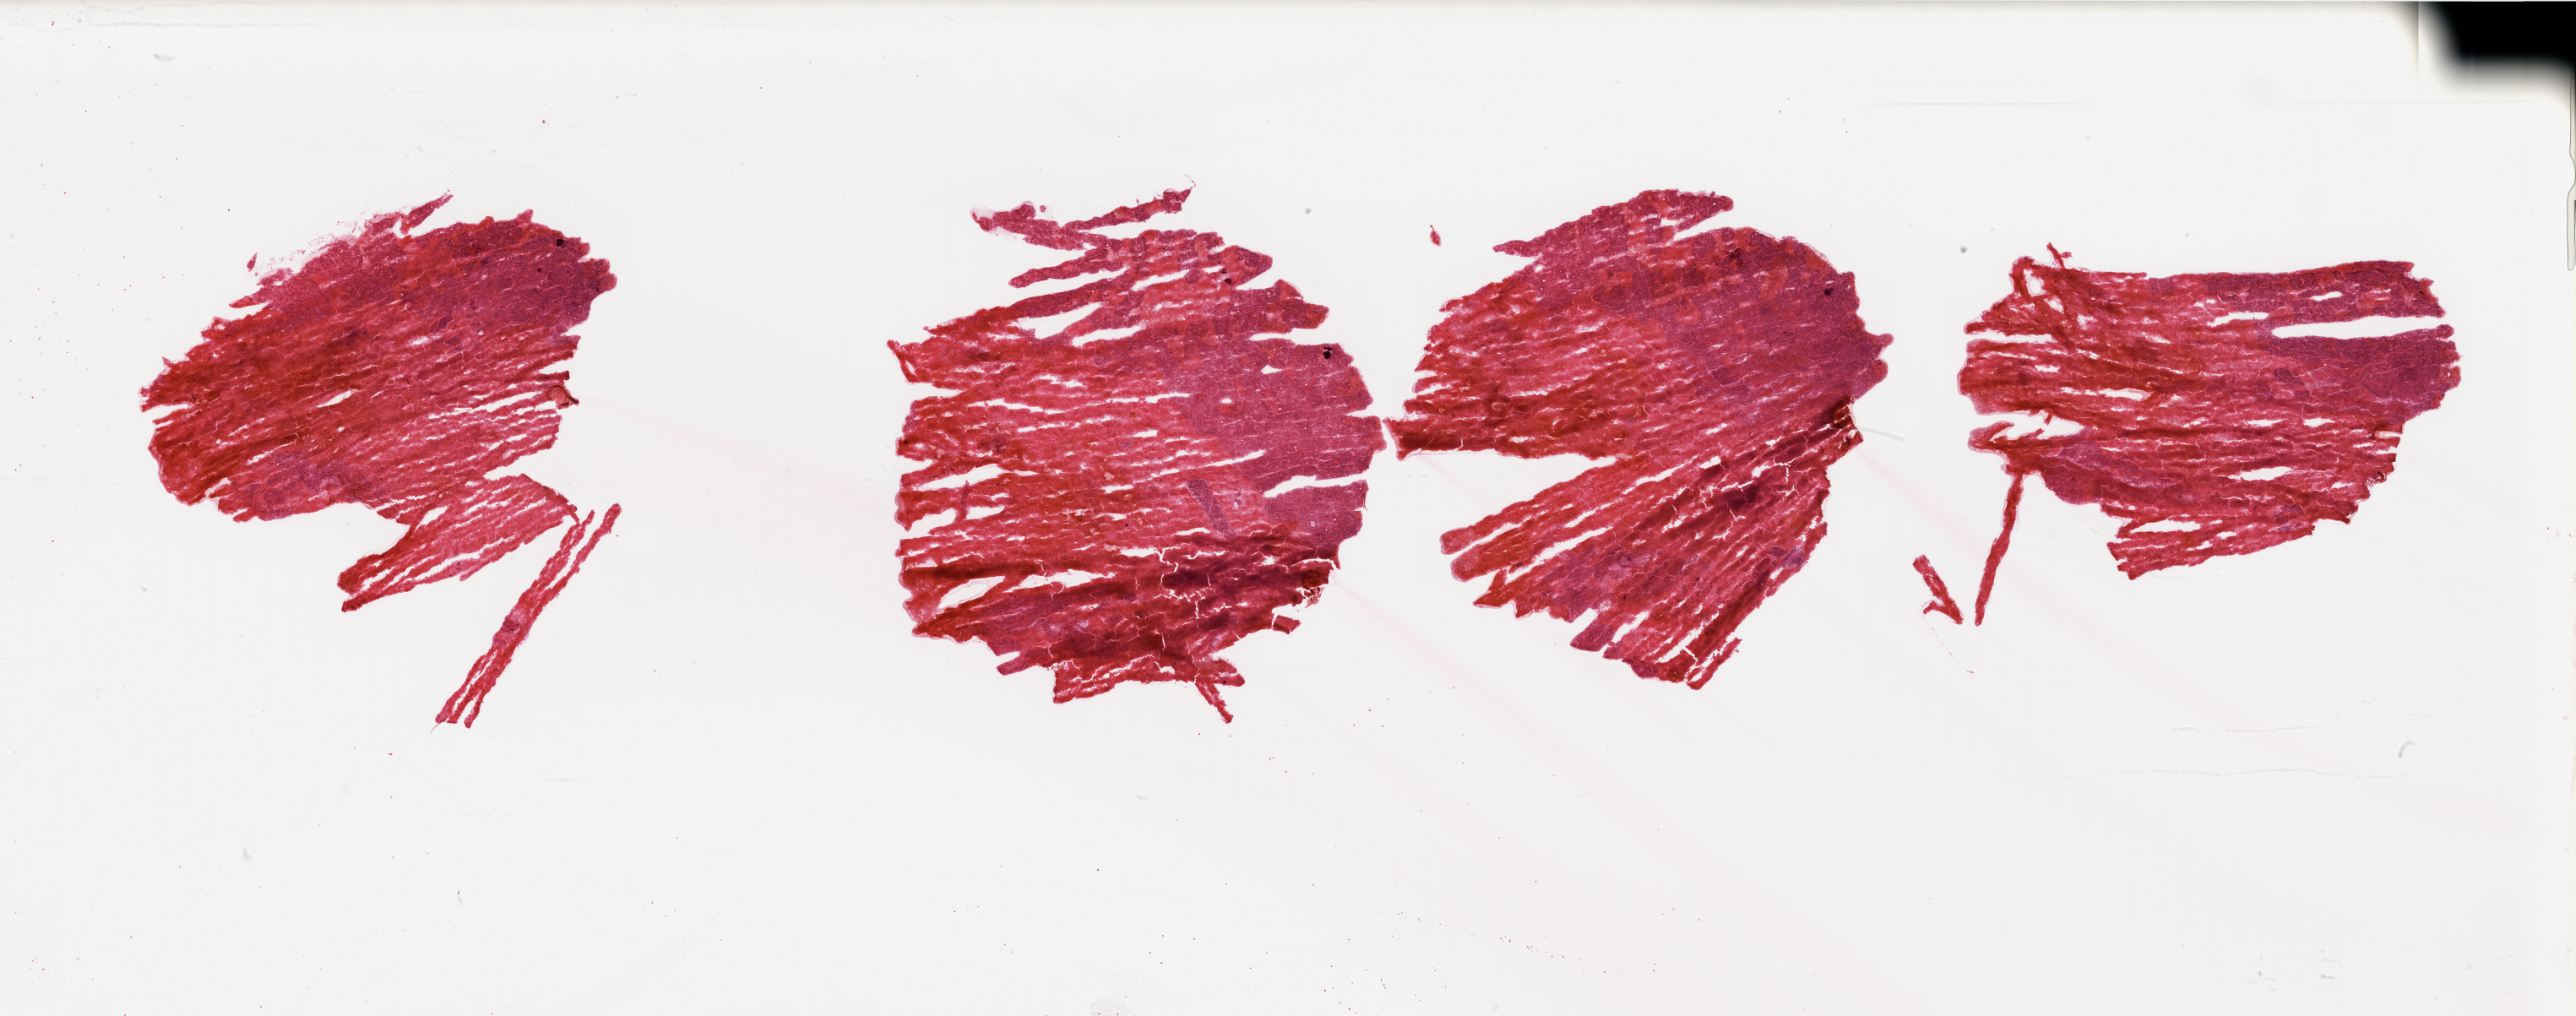
Whole-slide histology image, H&E-stained, shown as a low-resolution overview of the whole scanned area (about 48.2 x 19.0 mm, from a 20x scan). Kidney, tumour tissue. Female, 49 y/o. Histologic grade: G3 (poorly differentiated).
Diagnosis: Renal cell carcinoma, NOS. AJCC pathologic stage: II.